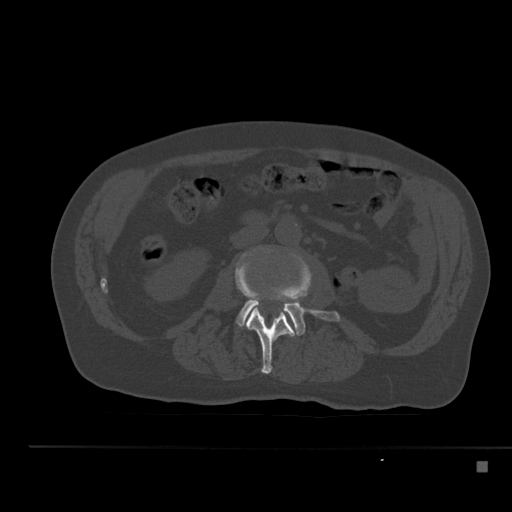
CT including the spine, one axial slice. Position 175 of 517 along the scan axis. Reconstruction kernel Br40s. 120 kVp. Bone window (W 1800 / L 400 HU). 512 × 512 image matrix, field of view 408 × 408 mm. Male patient, age 70 years. Case-level facts recorded for this patient, not image findings: primary cancer: renal; vertebrae with lytic lesions (as recorded): T4, T6, T10, T12, L3, L4, L5.
Annotated regions visible in this slice (semi-automatically segmented with operator editing):
- L2 vertebra: box from (x=235, y=257) to (x=295, y=374) px
- L3 vertebra: (x=237, y=269)–(x=340, y=336)